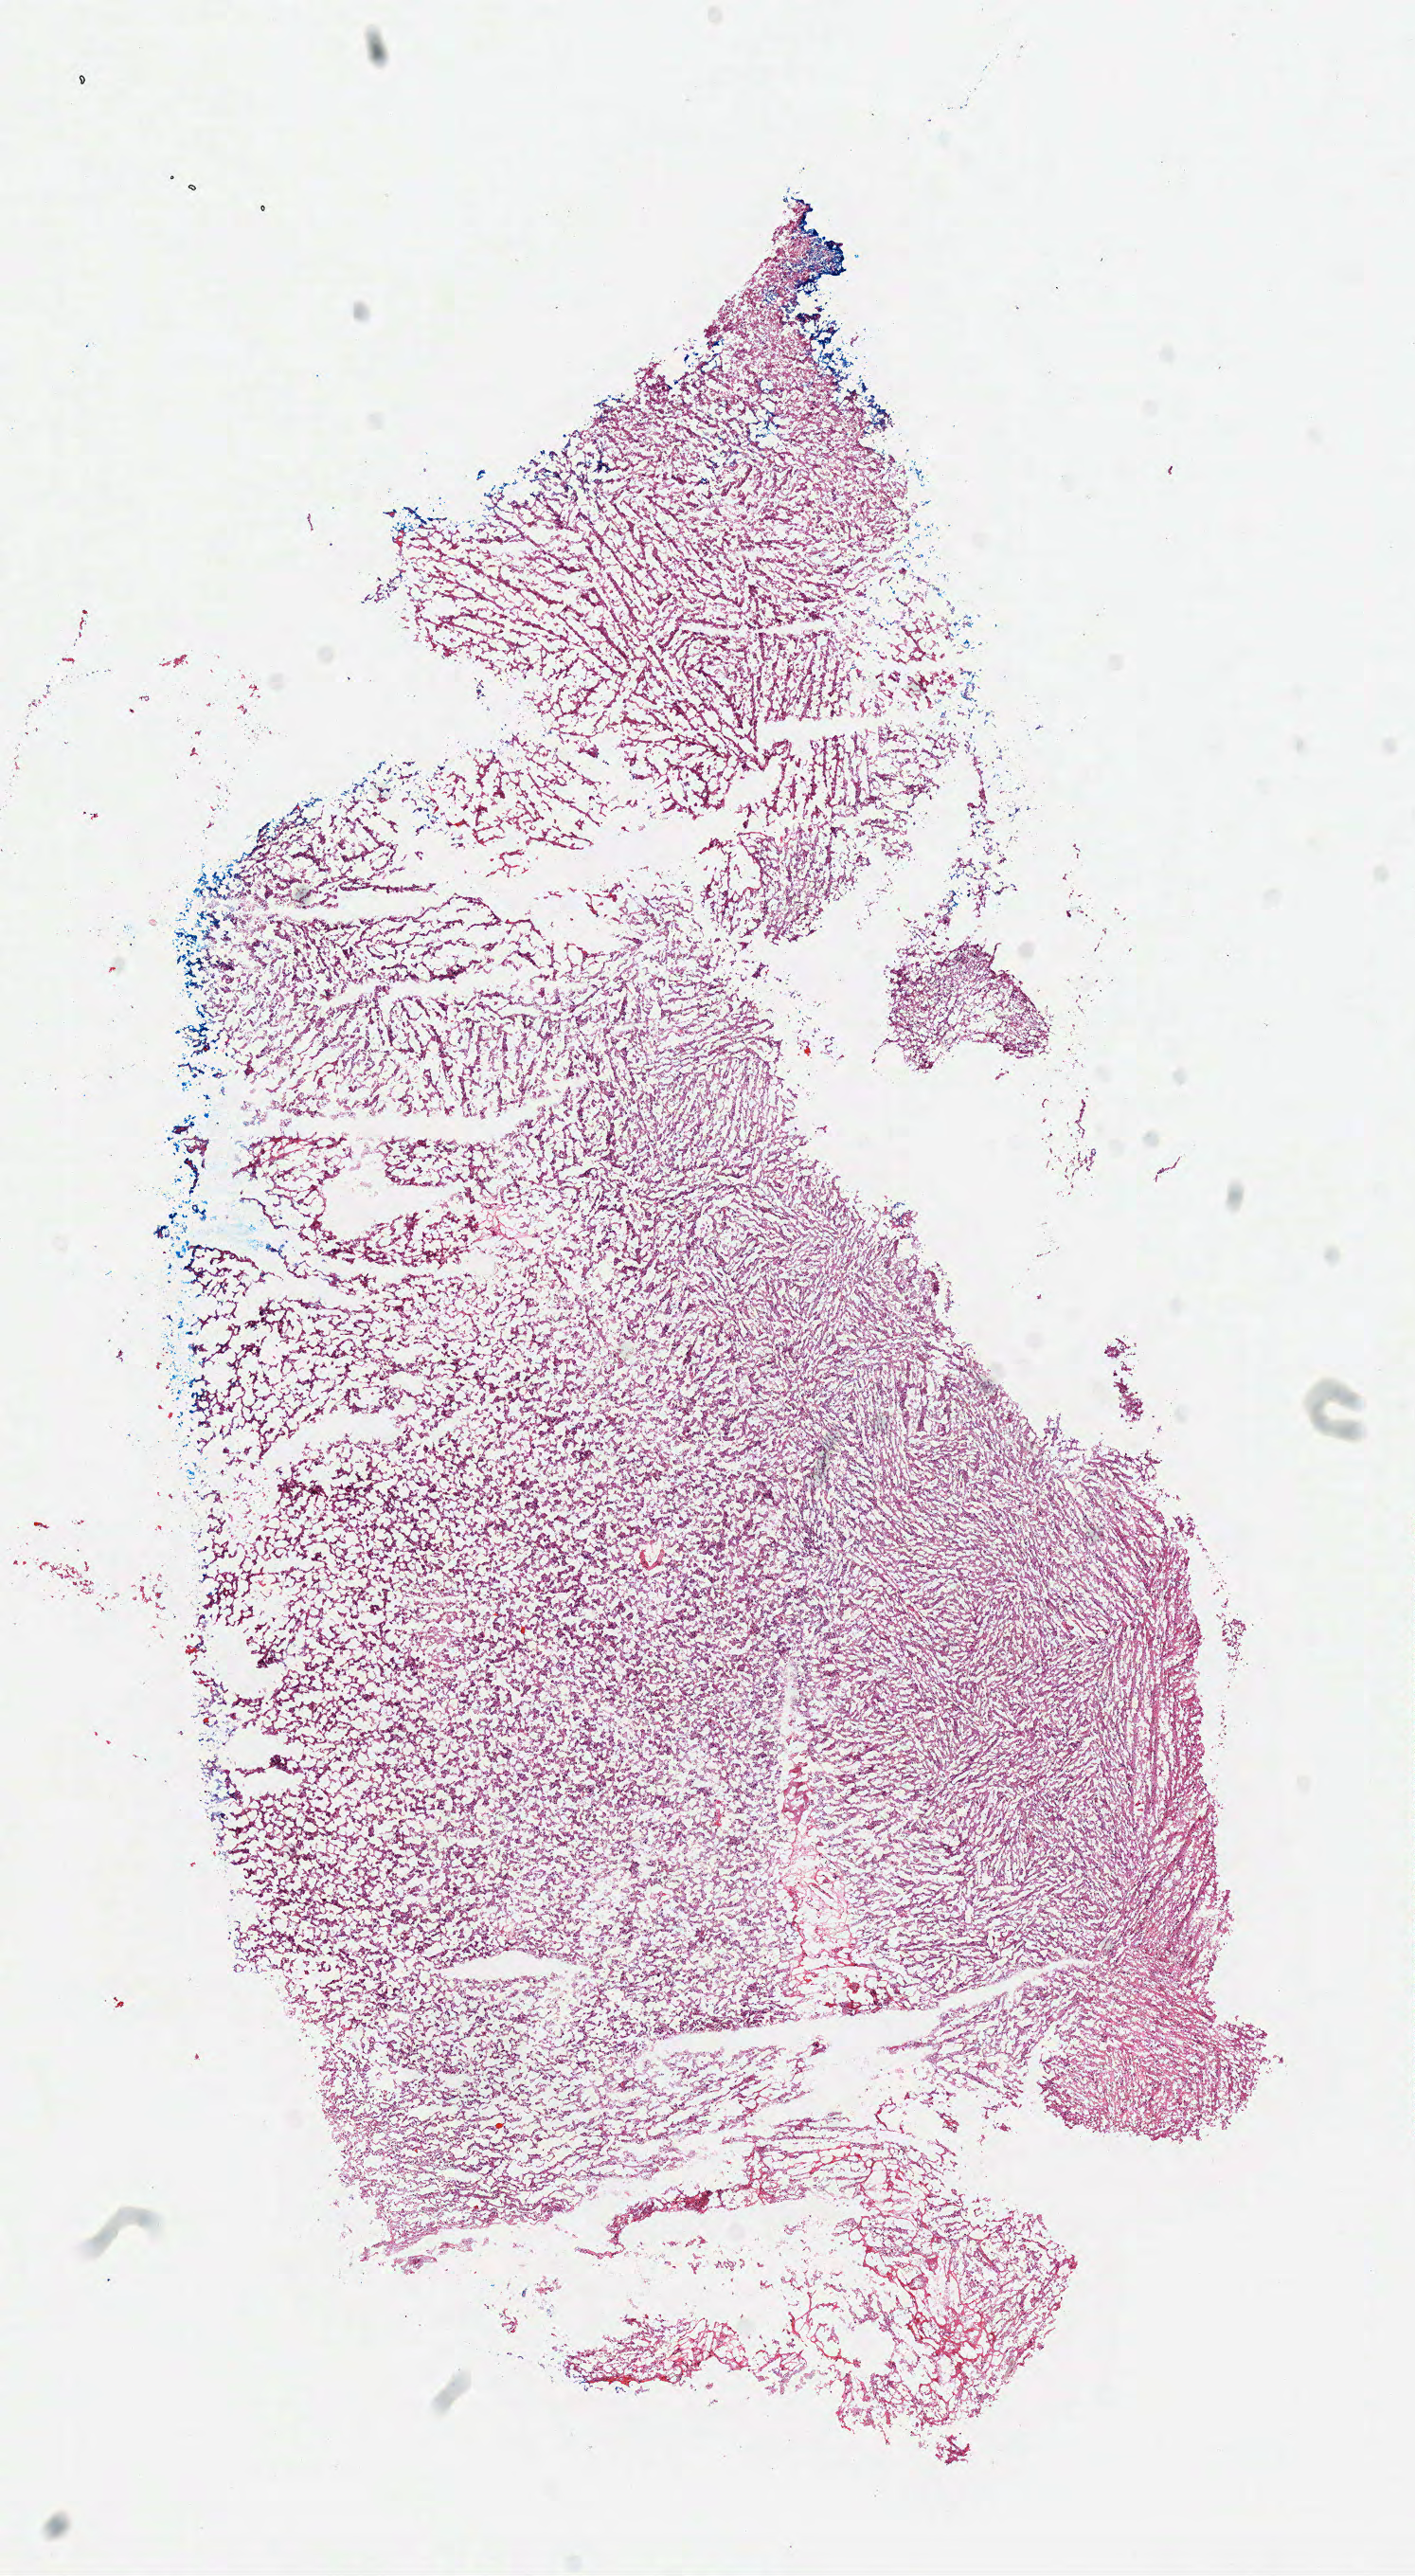
Digitized H&E tissue section (whole slide), shown as a low-resolution overview of the whole scanned area (about 5.9 x 10.7 mm, from a 40x scan), frozen section, sample: primary tumour, brain. Male patient; age at initial diagnosis 62 years. Histologic grade: G2 (moderately differentiated). Pathologist review of this section (percent, as recorded): tumour cells 100%, tumour nuclei 75%, normal cells 0%, stromal cells 0%, necrosis 0%.
Laterality: left. Pathologic diagnosis: Oligodendroglioma, NOS (cerebrum).